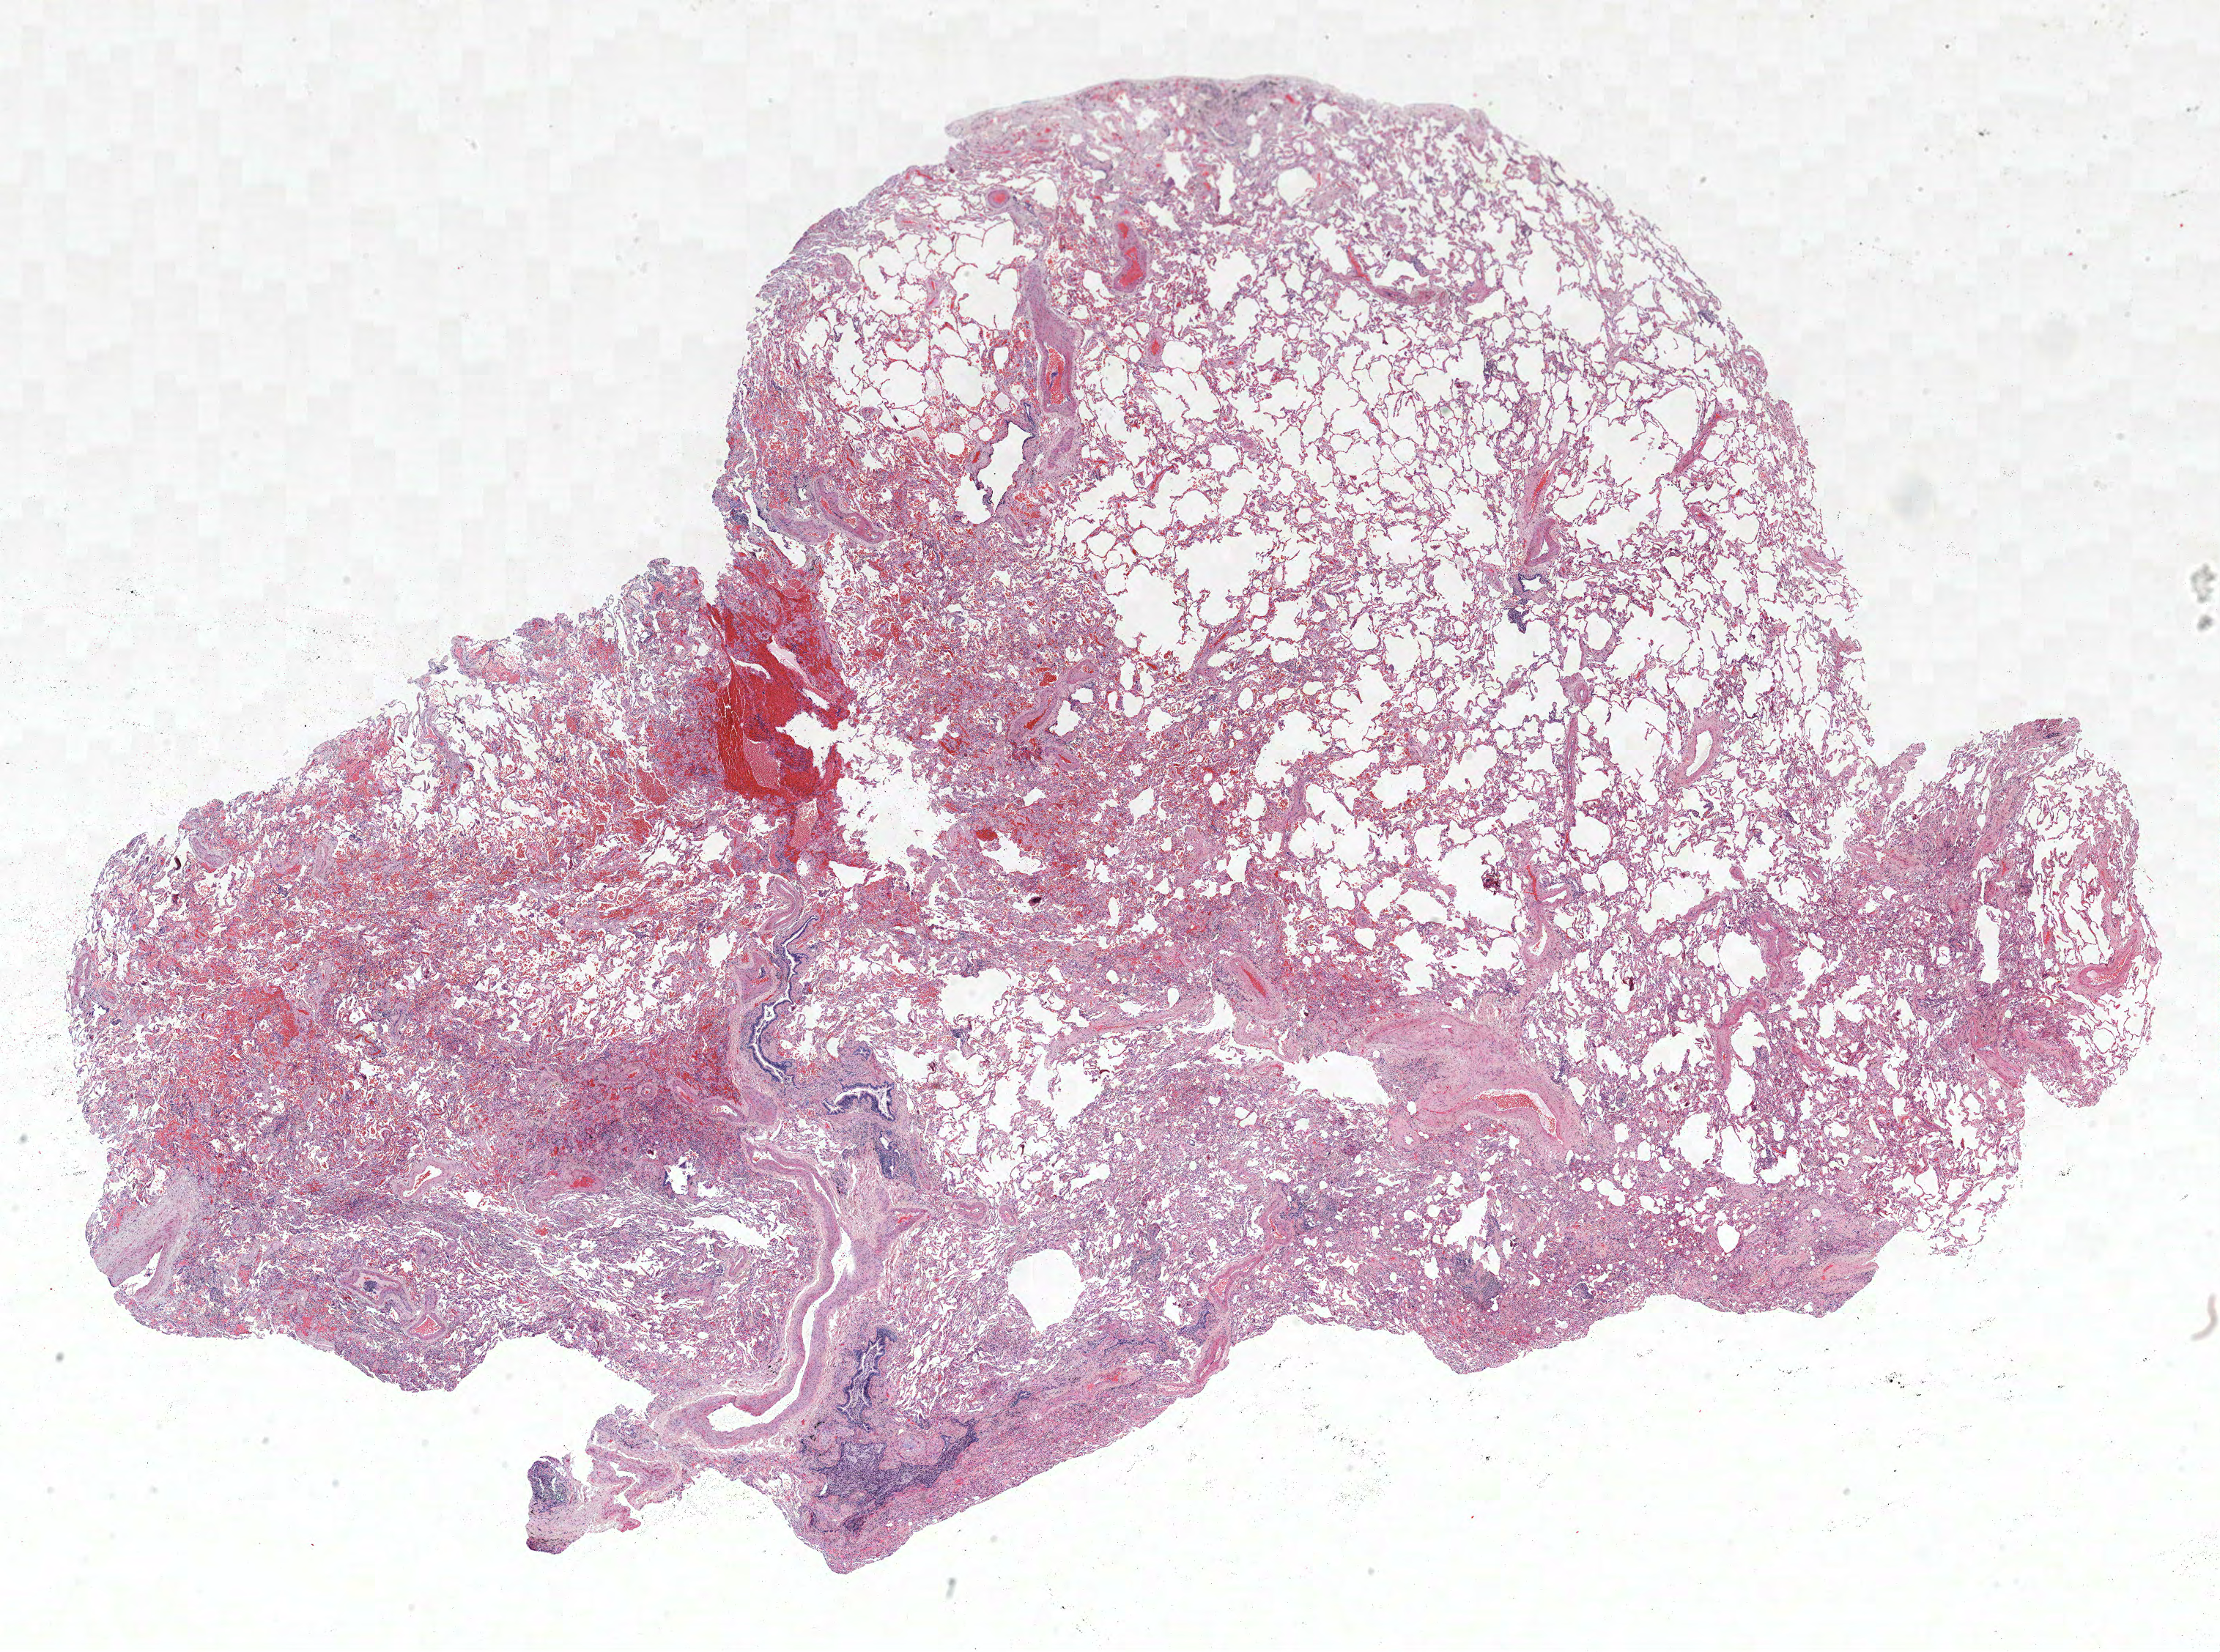
Whole-slide histology image, H&E-stained — low-resolution overview of the scanned area, about 24.2 x 18.0 mm (slide scanned at 40x). Formalin-fixed paraffin-embedded (FFPE) section. Lung tissue. Female patient, aged 64 at enrolment. Current smoker at enrolment.
Participant's lung-cancer diagnosis: Squamous cell carcinoma, NOS (ICD-O-3 8070/3).